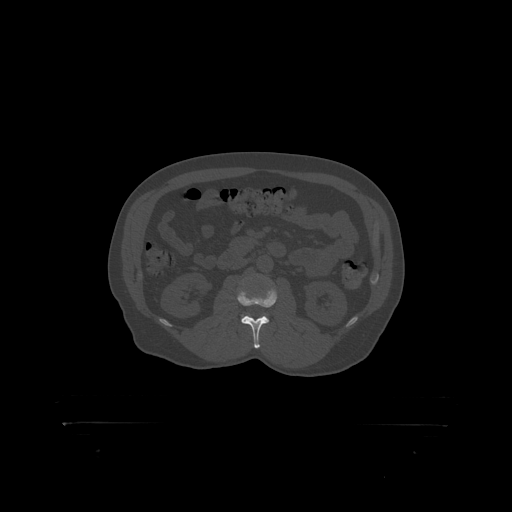
CT including the spine, one axial slice. Position 287 of 399 along the scan axis. Reconstruction kernel STANDARD. 120 kVp. Bone window (W 1800 / L 400 HU). 1.25 mm slice thickness. 512 × 512 image matrix. Male patient, age 46 years. Case-level facts recorded for this patient, not image findings: primary cancer: skin.
Outlined on this slice (semi-automatically segmented with operator editing):
- L2 vertebra: box from (x=238, y=289) to (x=277, y=319) px
- L3 vertebra: (x=242, y=315)–(x=266, y=317)